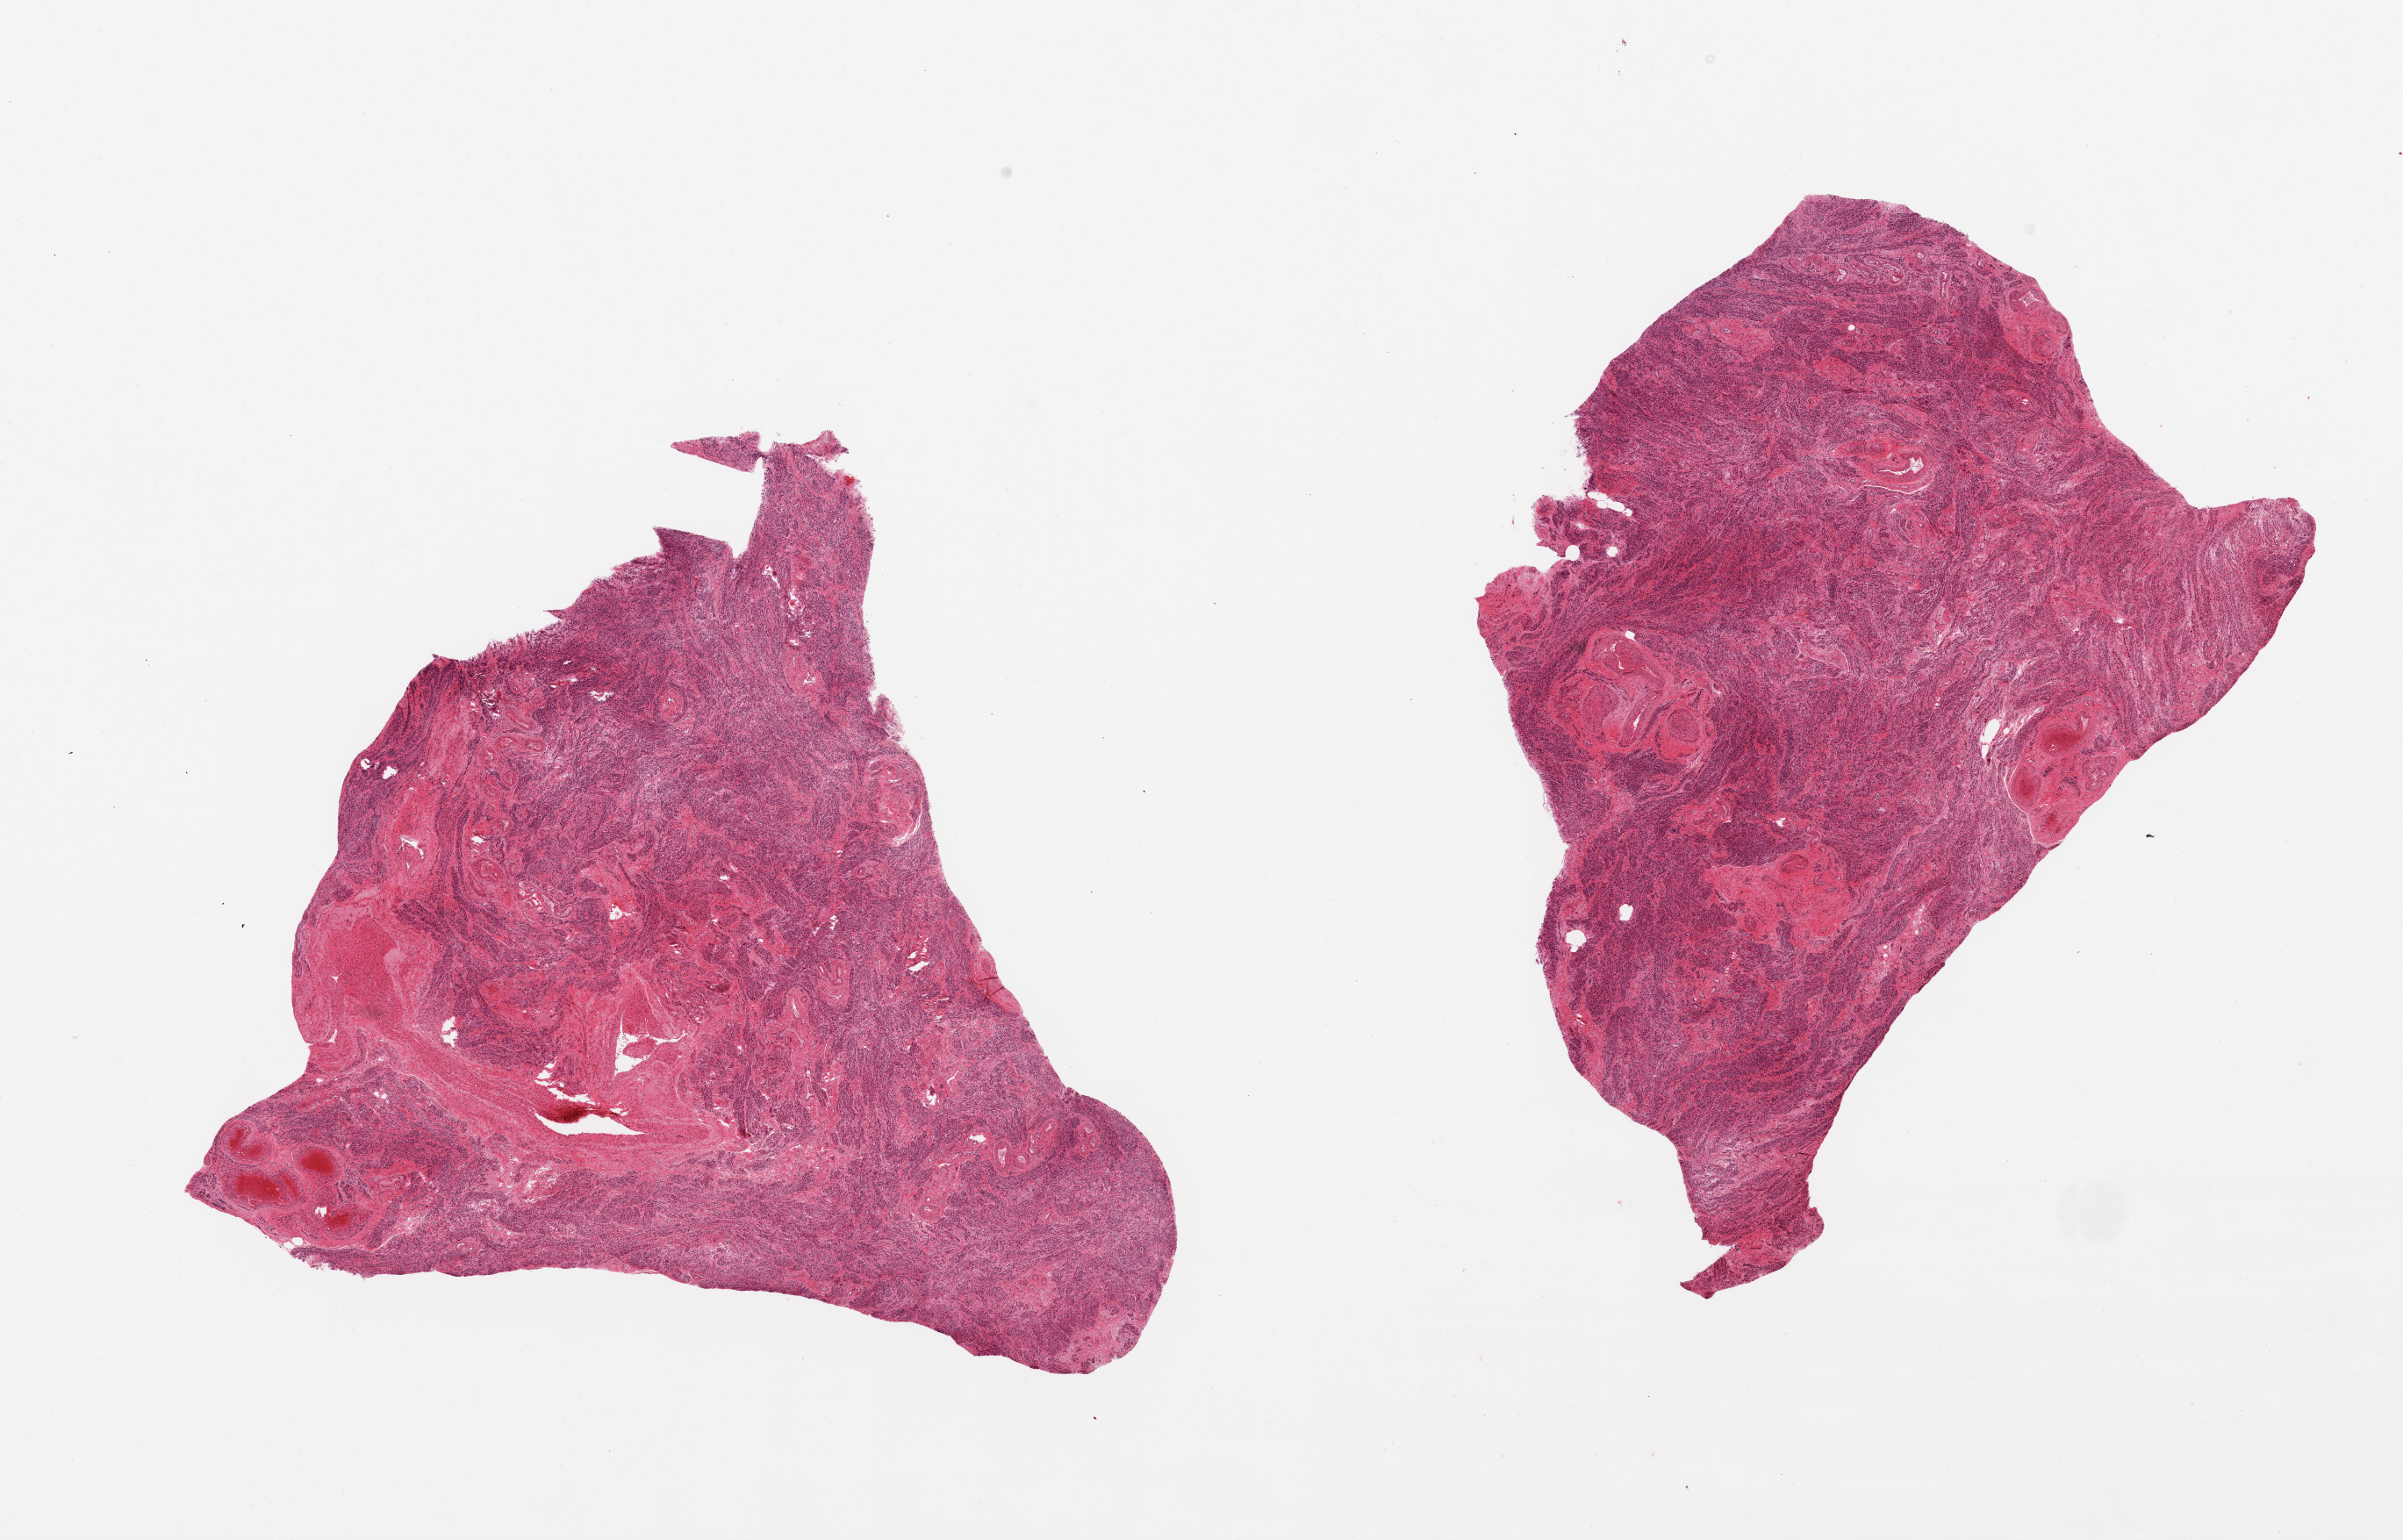
Digitized haematoxylin and eosin-stained section, brightfield, low-resolution overview of the scanned area, about 21.7 x 13.9 mm, PAXgene-fixed paraffin-embedded (PFPE) section, target tissue: uterus, donor tissue sample. Donor sex: female.
- pathologist's review note for this sample: 2 pieces; myometrium in these cuts